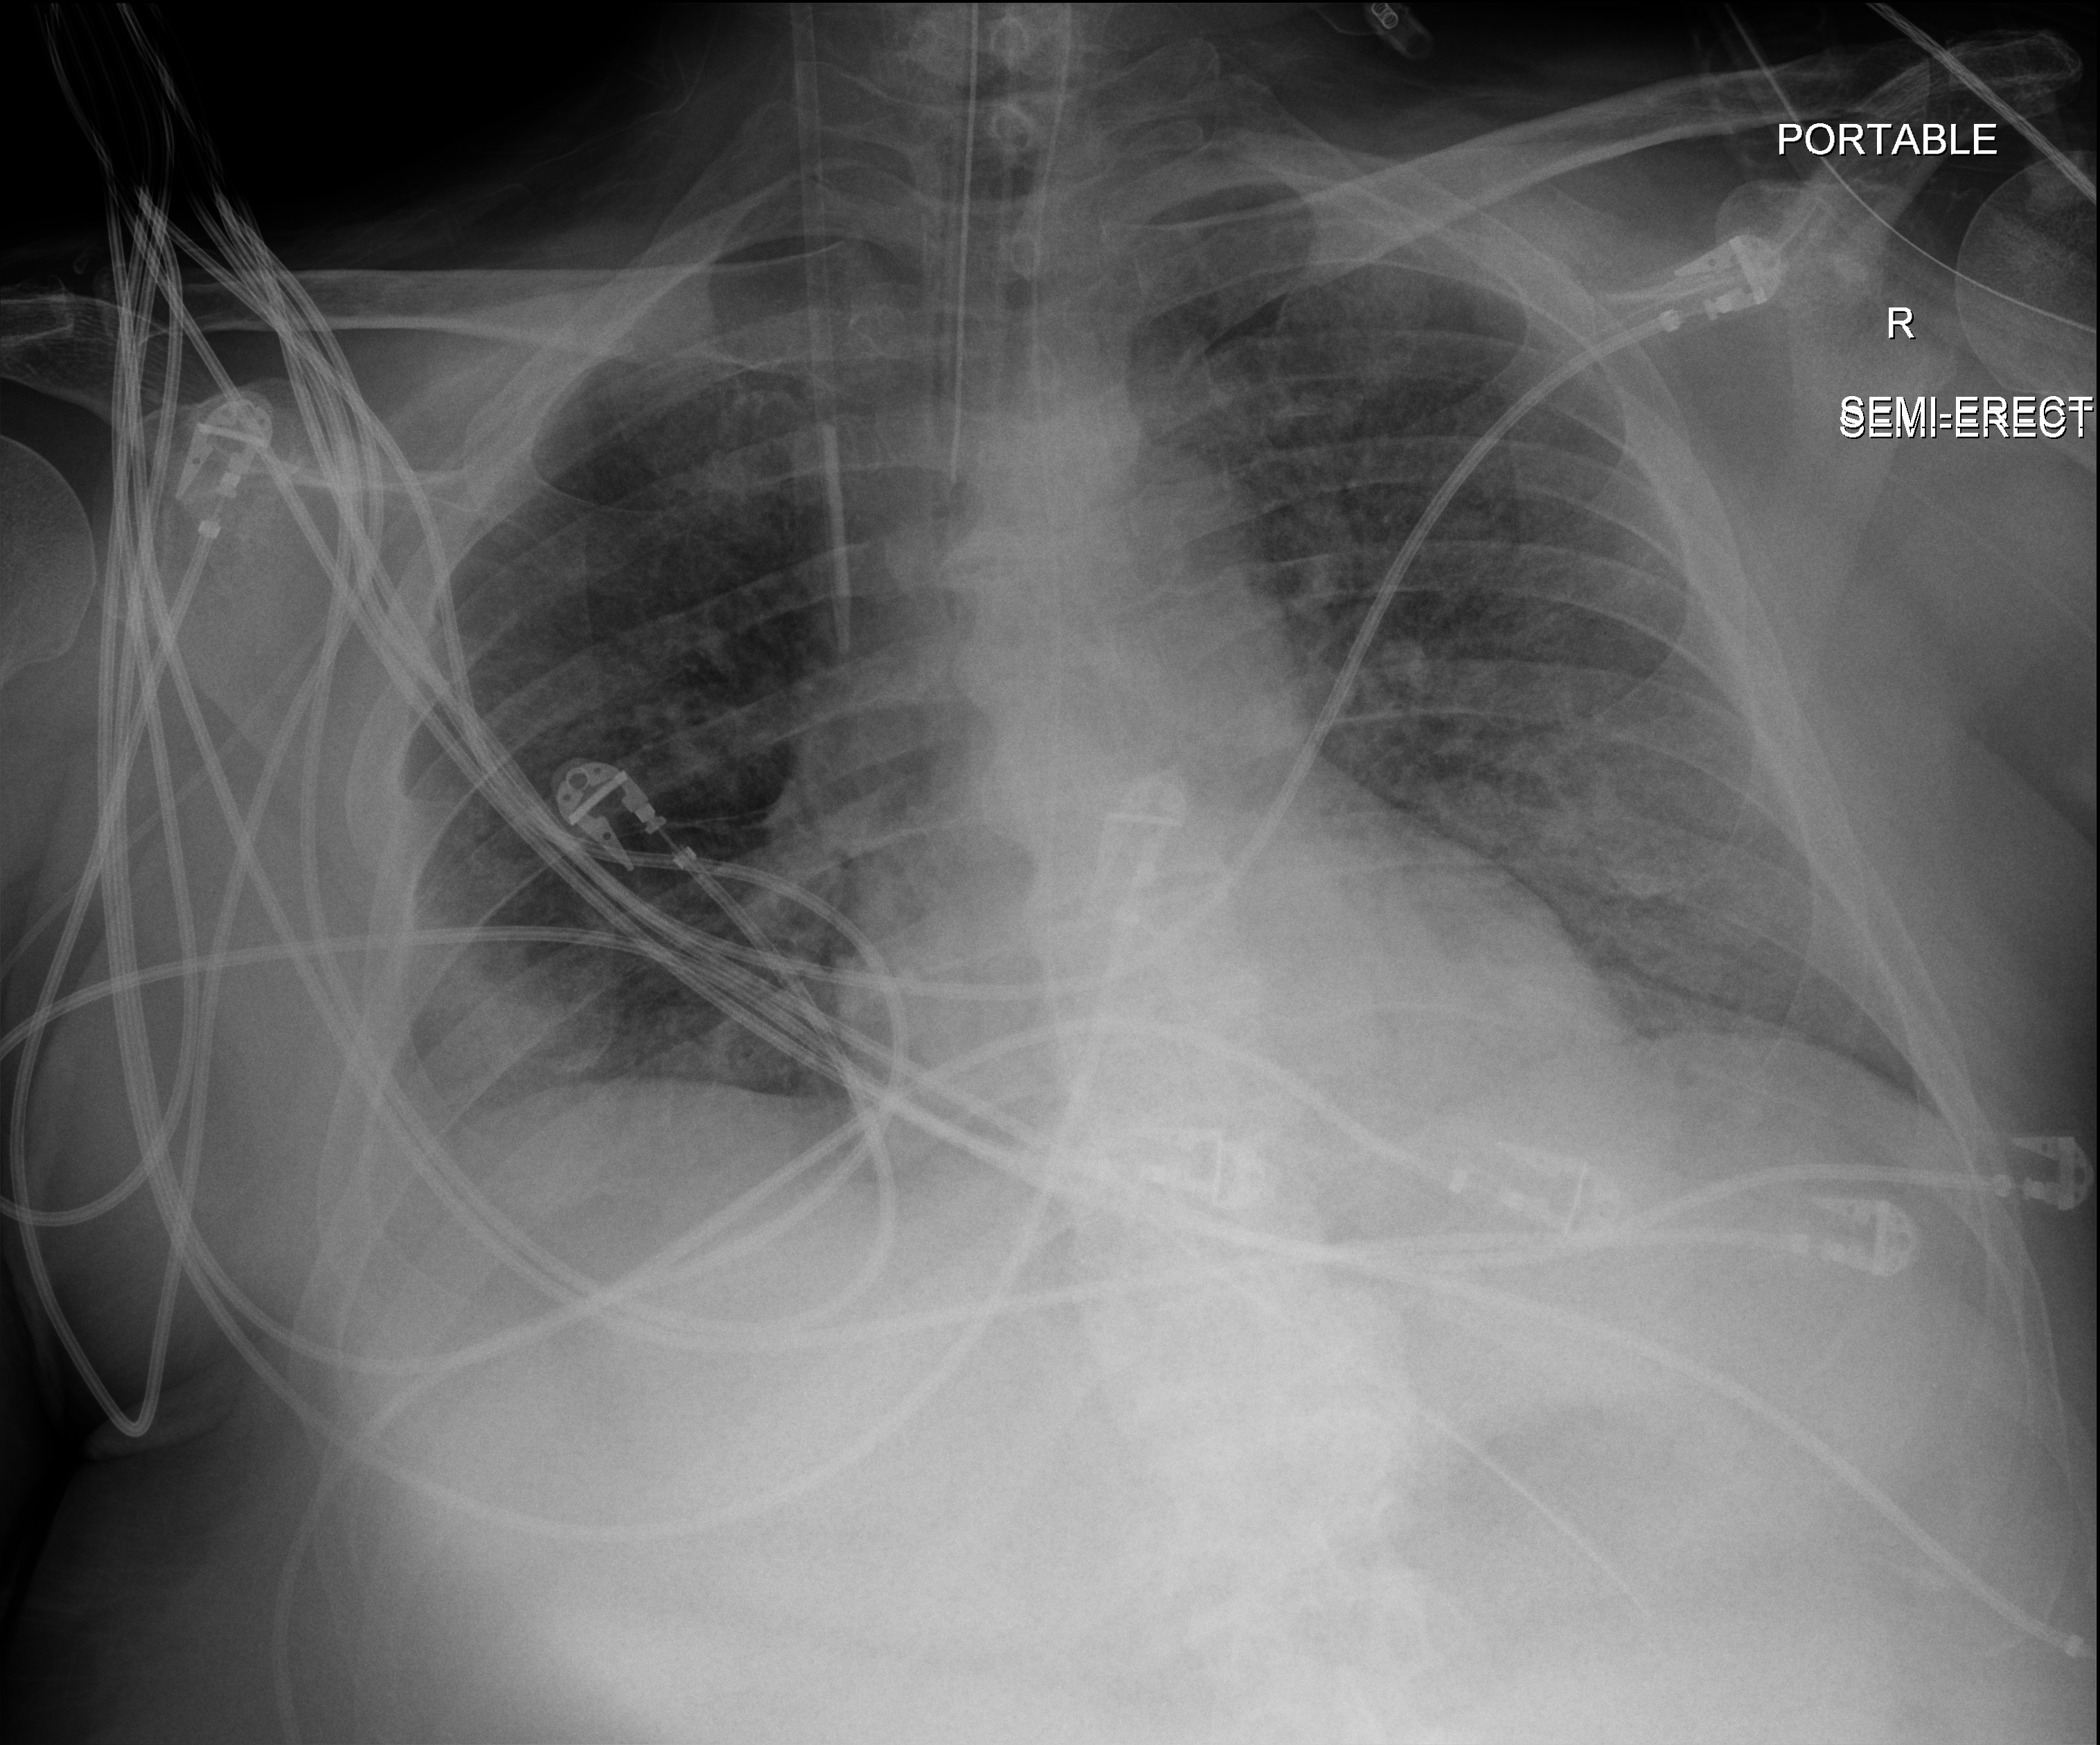
Chest X-ray (portable), anteroposterior (AP) projection. Patient hospitalised with COVID-19; male, aged 60–74 years.
Admission-level facts for this patient (not findings on this image; timing relative to this image not recorded): chronic kidney disease (admission record): no; admitted to intensive care during this hospital stay: yes.